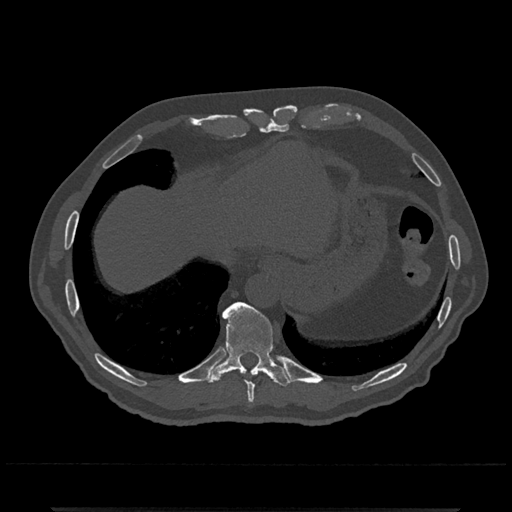
CT including the spine, one axial slice. Position 572 of 797 along the scan axis. 120 kVp. Bone window (W 1800 / L 400 HU). 0.5 mm slice thickness. 512 × 512 image matrix, field of view 393 × 393 mm. Male patient, age 67 years. Case-level facts recorded for this patient, not image findings: primary cancer: prostate.
Structures marked on this image (semi-automatic segmentation, software-assisted and operator-edited):
- T10 vertebra: bounding box [x1, y1, x2, y2] px = [207, 302, 291, 387]
- T9 vertebra: [246, 381, 254, 404]